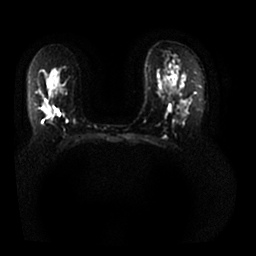
Breast MRI, one axial slice. Slice 19 of 25 in the series (ordered by position). Diffusion-weighted series; image 2 of 4 stored at this slice position (different b-values; order by instance number). 1.5 T. 256 × 256 image matrix. Female patient.
Outlined on this slice (outlined manually by an expert reader):
- tumour on diffusion-weighted imaging: bounding box <46,110,52,118> (left, top, right, bottom; pixels)